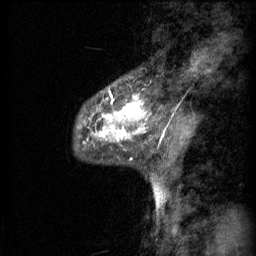
Breast MRI (dynamic contrast-enhanced), one sagittal slice; slice 18 of 60 in the series (ordered by position); 3 images stored at this slice position (order not interpretable as contrast timing); 1.5 T; TE 4.2 ms, TR 11 ms; 2 mm slice thickness; 256 × 256 image matrix, field of view 200 × 200 mm. Female patient, age 48 years.
Annotated regions visible in this slice (semi-automatic segmentation, software-assisted and operator-edited):
- analysis volume of interest (the breast-tissue region the enhancement analysis was run in; not a lesion): bounding box <82,80,149,143> (left, top, right, bottom; pixels)
- tumour enhancement mask (voxels above the 70 % enhancement threshold inside the analysis volume of interest): <96,94,146,141>